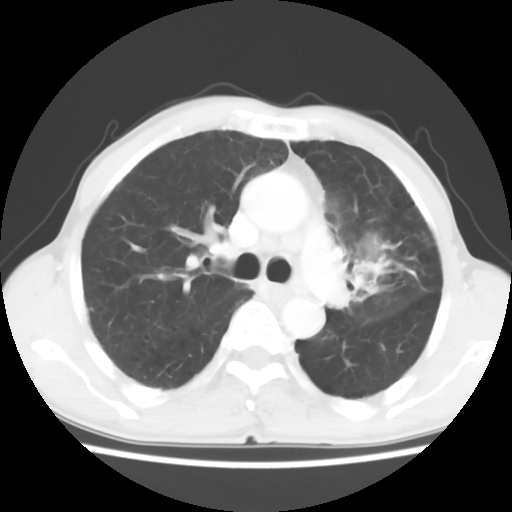
Chest CT, one axial slice; position 38 of 60 along the scan axis; reconstruction kernel STANDARD; 120 kVp; lung window (W 1500 / L -600 HU); 5 mm slice thickness; 512 × 512 image matrix. Patient: male, 64 years. From the clinical record (not read from this slice): clinical TNM (as recorded): T3 N3 M0.
Outlined on this slice (rectangle marked by the reading radiologist):
- lung tumour (recorded histology: adenocarcinoma): bounding box [x1, y1, x2, y2] px = [345, 224, 403, 320]